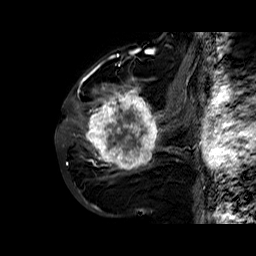
Breast MRI (dynamic contrast-enhanced), one sagittal slice. Position 31 of 60 along the scan axis. Dynamic contrast-enhanced series, time point 2 of 6 at this slice position (early post-contrast). 1.5 T. TE 6.4 ms, TR 32.8 ms. 256 × 256 image matrix, field of view 200 × 200 mm. Female patient. From the clinical record (not read from this slice): setting: breast cancer imaged before/during neoadjuvant chemotherapy; receptor status: HR-positive, HER2-negative.
Structures marked on this image (semi-automatically segmented with operator editing):
- analysis volume of interest (the breast-tissue region the enhancement analysis was run in; not a lesion): bounding box <86,77,163,177> (left, top, right, bottom; pixels)
- tumour enhancement mask (voxels above the 100 % enhancement threshold inside the analysis volume of interest): <86,78,162,170>